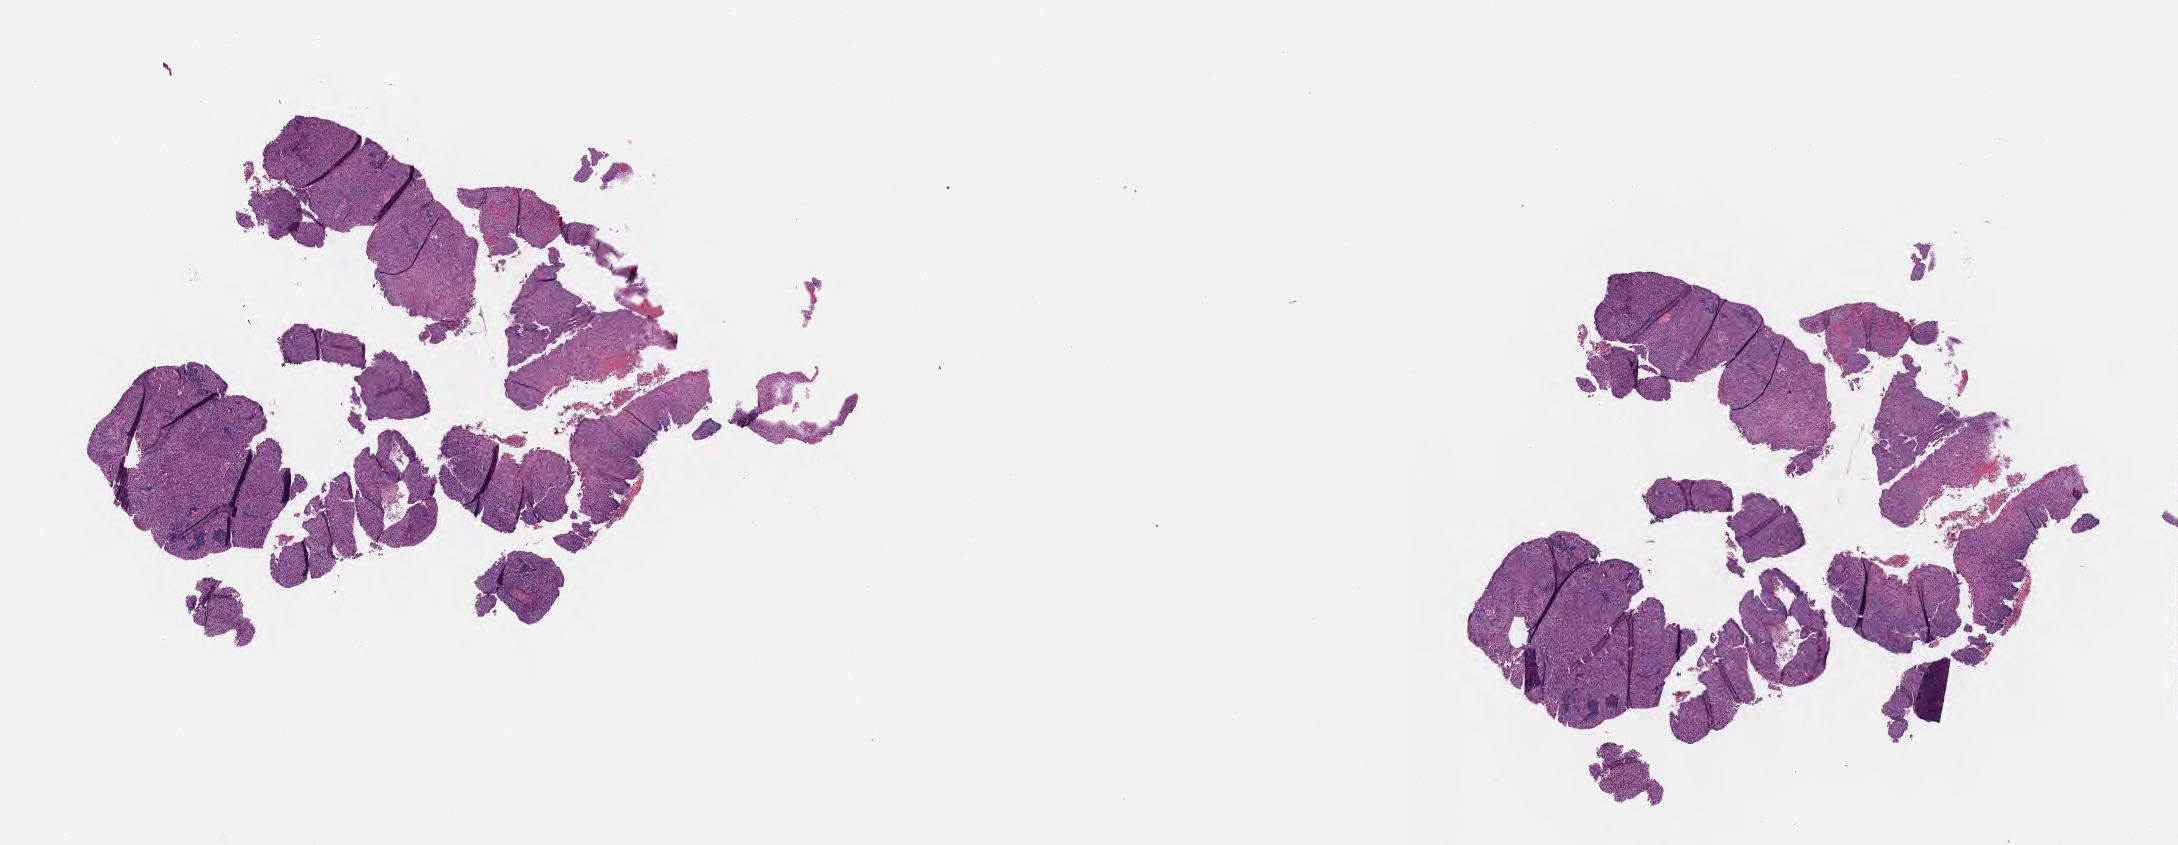
H&E whole-slide image — a low-resolution overview of the entire scanned area, about 17.6 x 6.8 mm; specimen: tumor tissue; site: cervix. Patient: female, age 37 years.
Histologic diagnosis: Squamous cell carcinoma, large cell, nonkeratinizing, NOS.